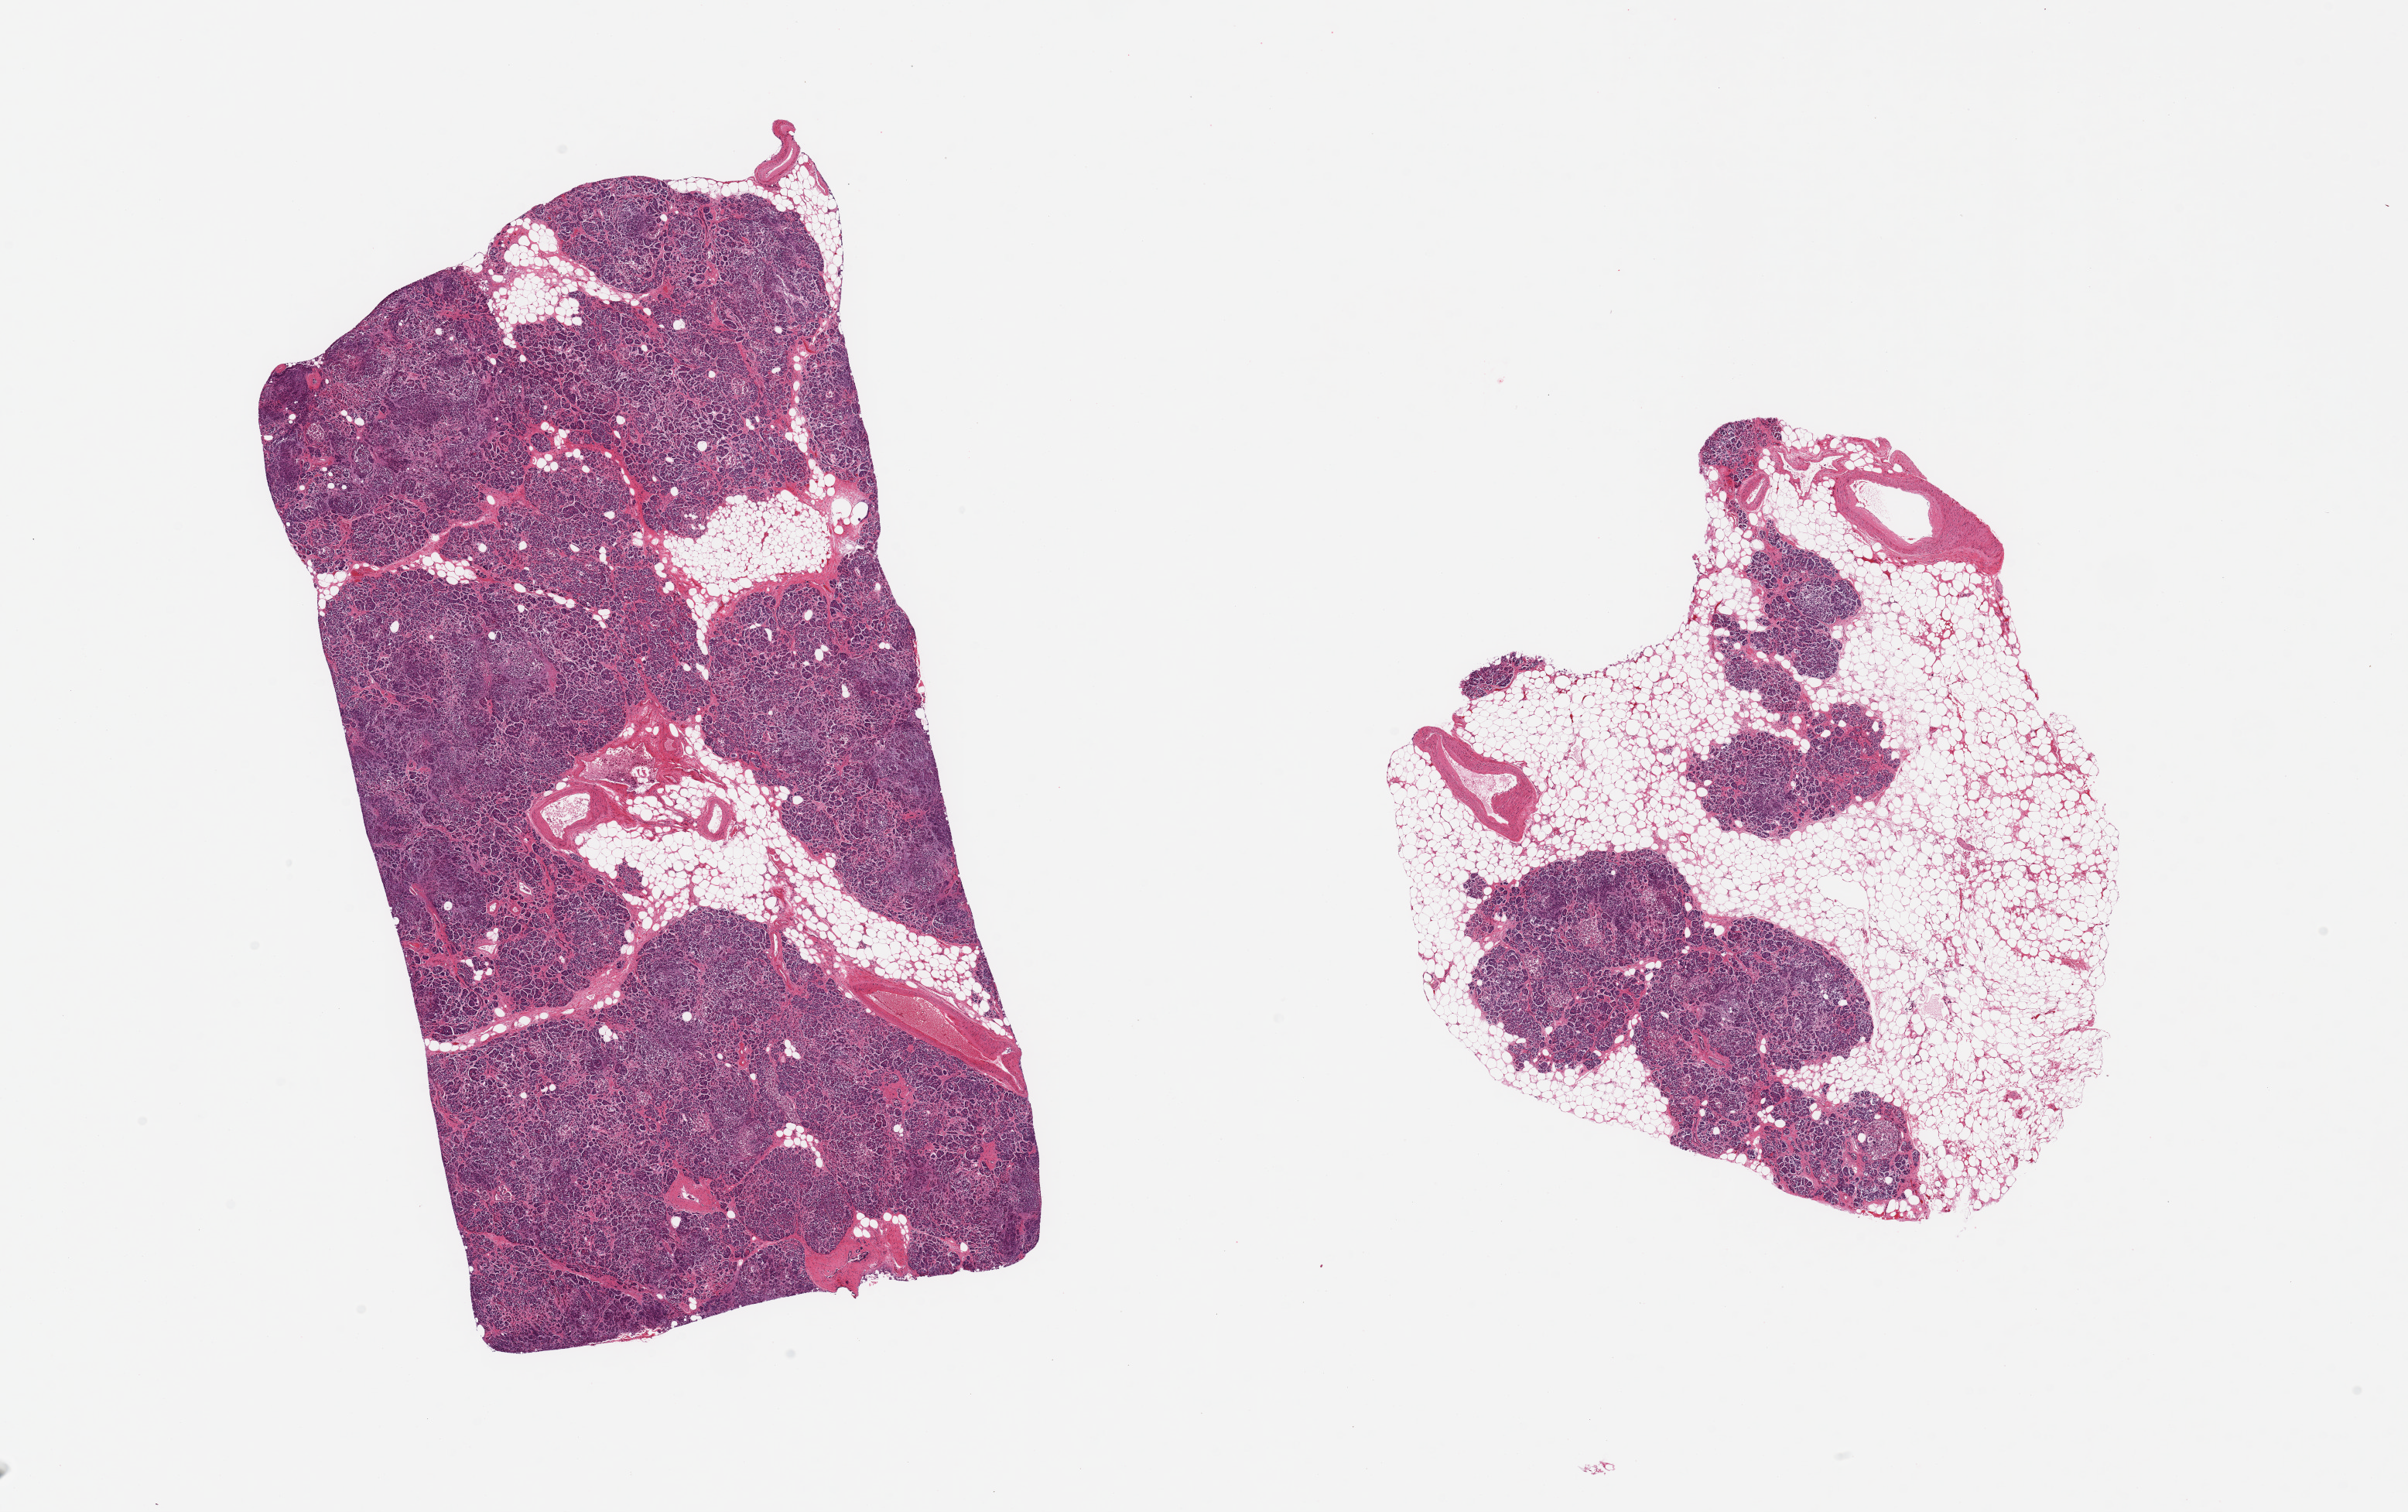
Whole-slide image, H&E stain — whole scanned area (about 24.6 x 15.5 mm) shown as a low-resolution overview, PAXgene-fixed paraffin-embedded (PFPE) section, sampled site (target tissue): pancreas, donor tissue sample.
* review note (as recorded): 2 pieces, moderate-advanced saponification; islets barely visible, advanced degradation